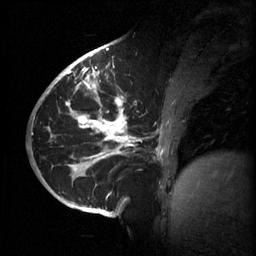
Breast MRI (dynamic contrast-enhanced), one sagittal slice. Slice 25 of 60 in the series (ordered by position). 3 images stored at this slice position (order not interpretable as contrast timing). 1.5 T. TE 4.2 ms, TR 11 ms. 256 × 256 image matrix. Female patient, age 51 years.
Outlined on this slice (semi-automatic segmentation, software-assisted and operator-edited):
- analysis volume of interest (the breast-tissue region the enhancement analysis was run in; not a lesion): bounding box <63,80,187,201> (left, top, right, bottom; pixels)
- tumour enhancement mask (voxels above the 70 % enhancement threshold inside the analysis volume of interest): <66,80,165,199>